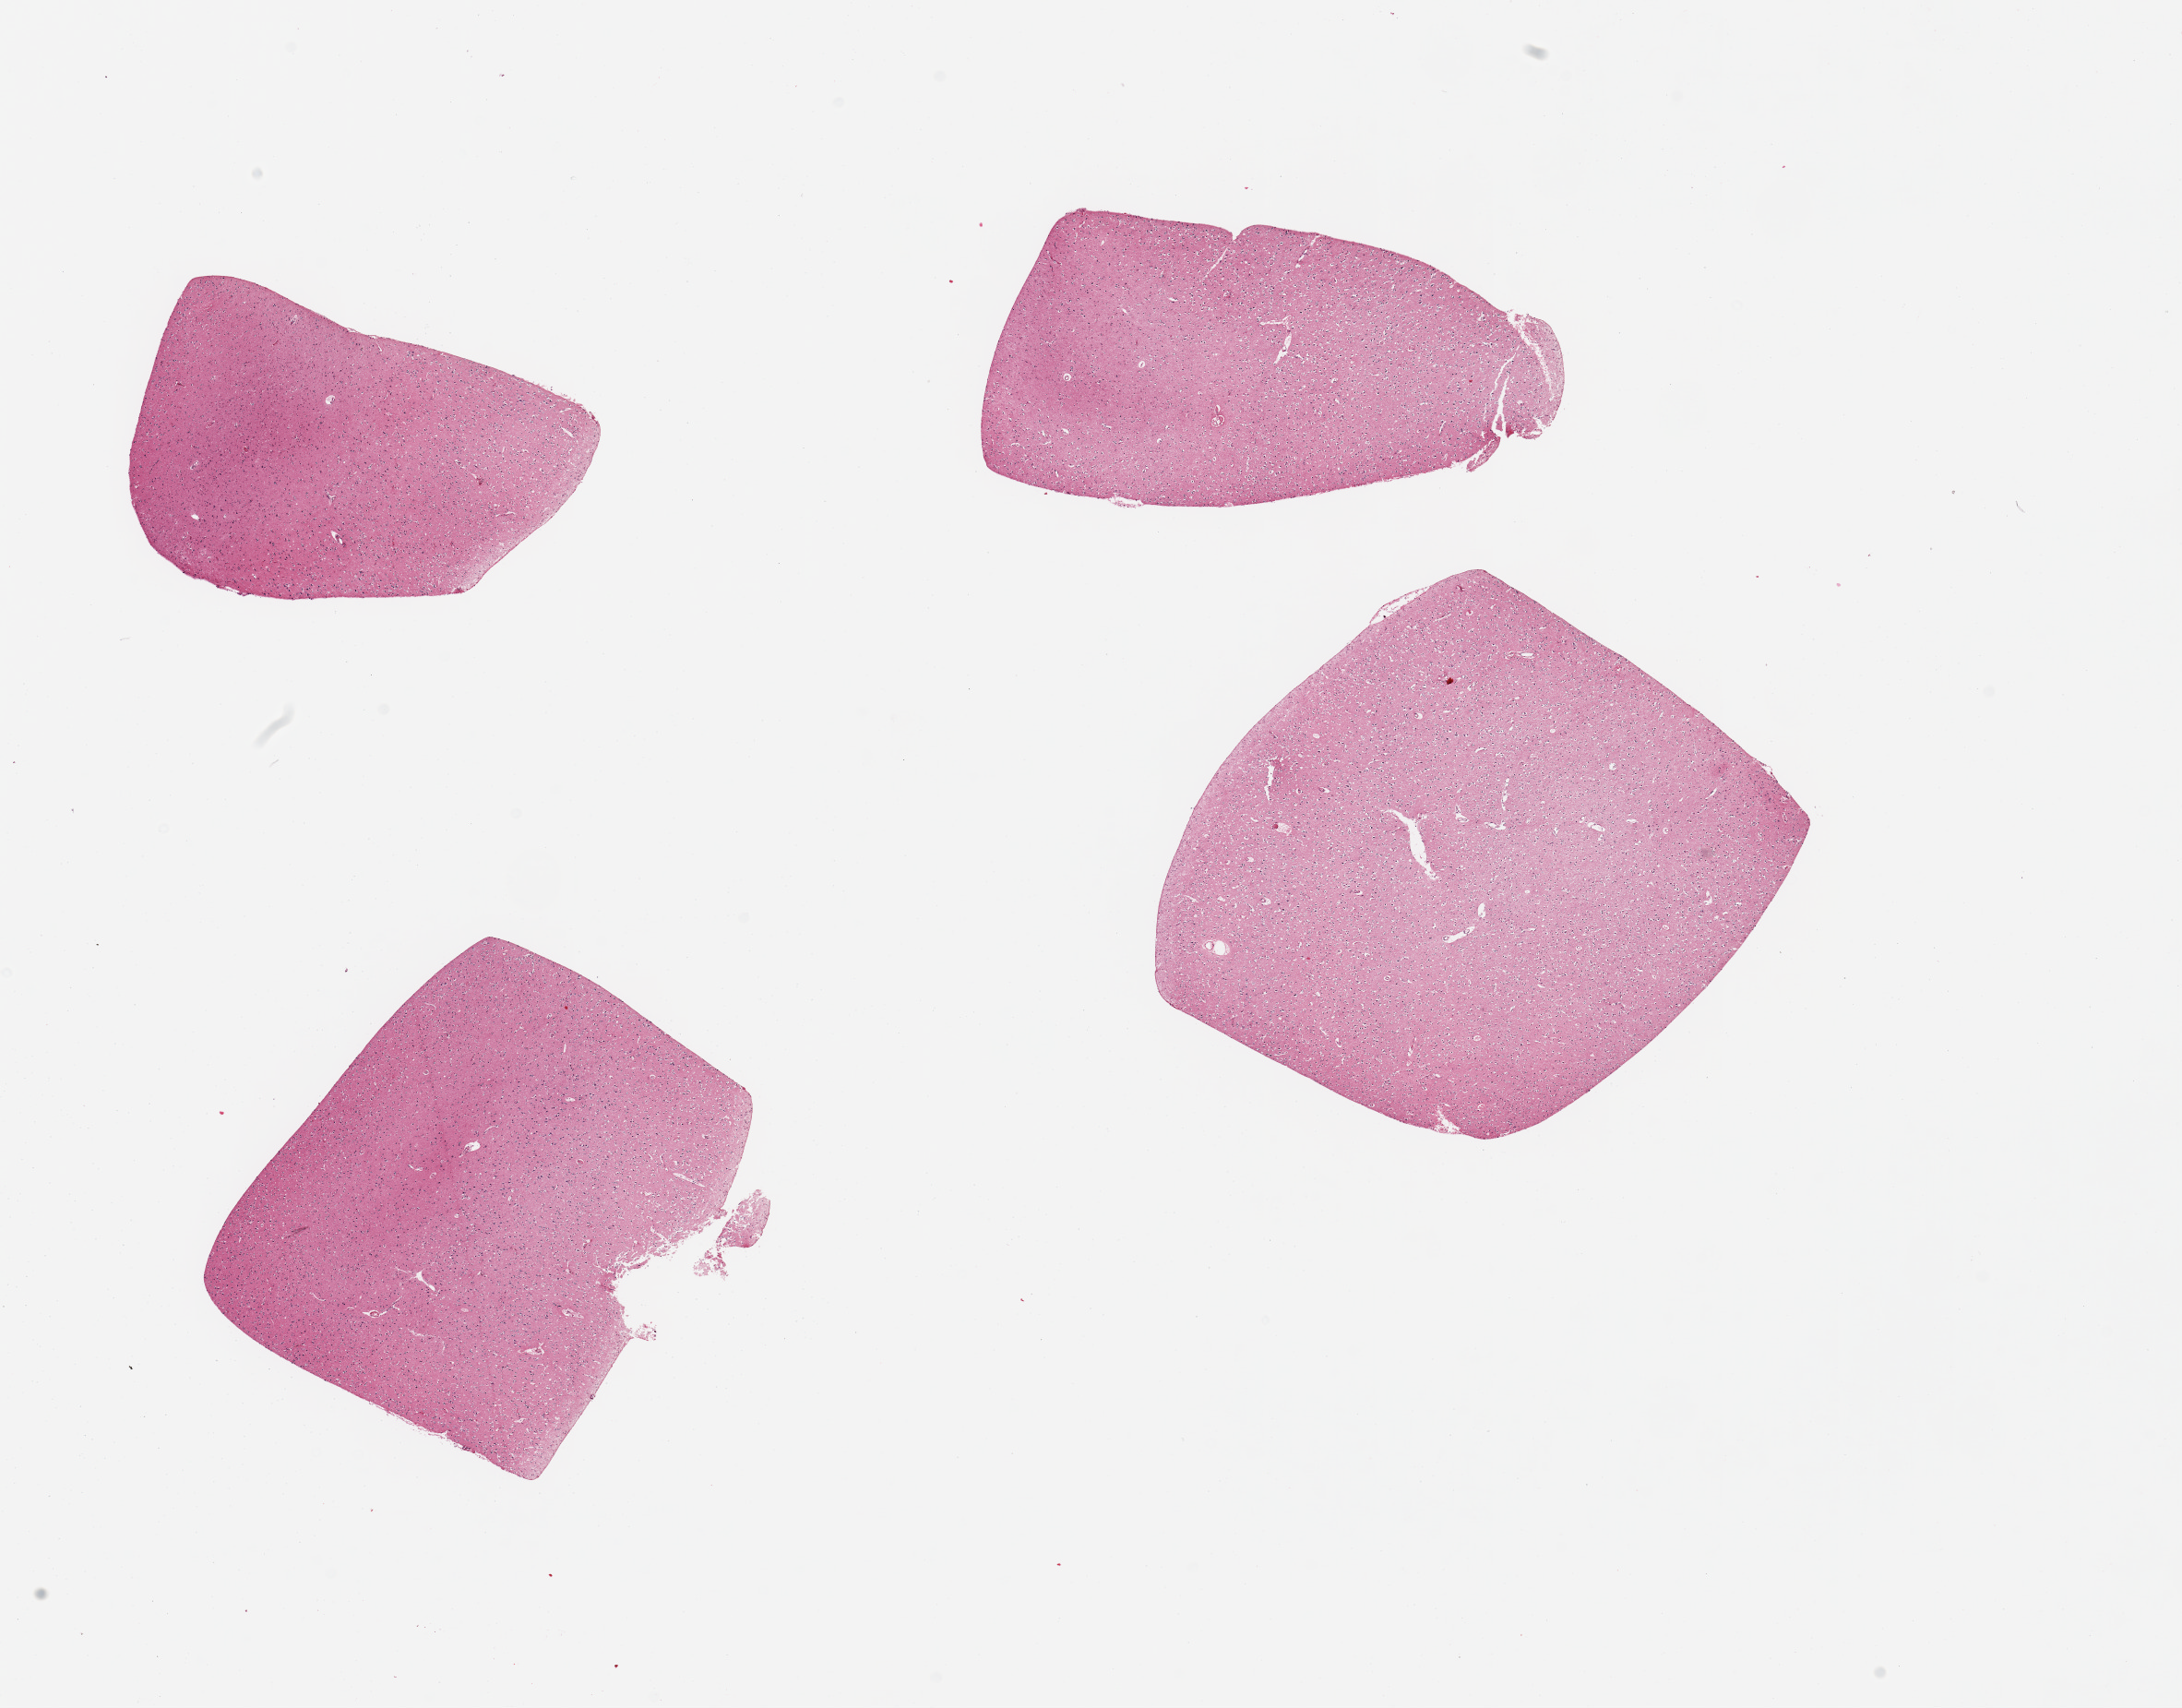
Digitized haematoxylin and eosin-stained section, low-resolution overview of the scanned area, about 18.7 x 14.6 mm (from a 20x scan), PAXgene-fixed, paraffin-embedded tissue, section of cerebral cortex (target tissue), donor tissue sample. Donor sex: male.
Reviewer comment on this tissue sample: 4 pieces.